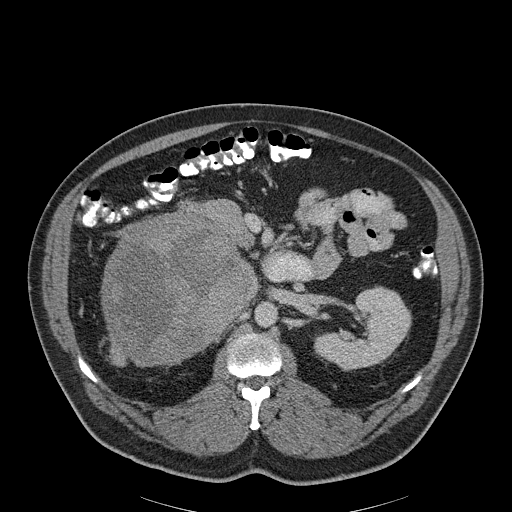
Contrast-enhanced abdominal CT, one axial slice; slice 118 of 186 in the series (ordered by position); soft-tissue window (W 400 / L 40 HU); 3 mm slice thickness; 512 × 512 image matrix. Patient: male, 56 years. From the clinical record (not read from this slice): diagnosis: adrenocortical carcinoma; tumour side: right adrenal; tumour size at pathology: 18 cm; Ki-67 index: 2 %; stage (as recorded): 3.
Annotated regions visible in this slice (semi-automatically segmented with operator editing):
- mass: bounding box (x1, y1, x2, y2) in pixels: (103, 217, 243, 363)